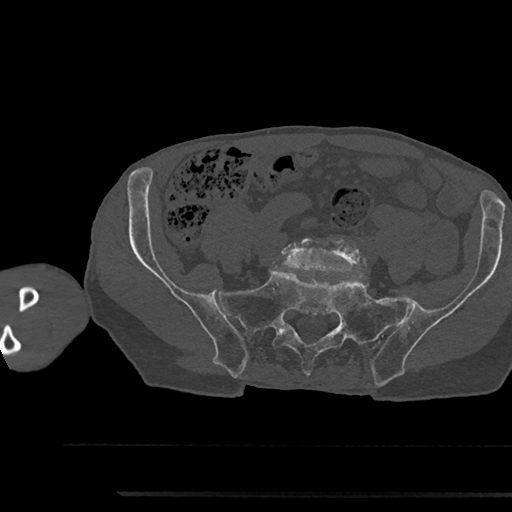
CT including the spine, one axial slice; position 298 of 797 along the scan axis; reconstruction kernel Br40s/3; 120 kVp; bone window (W 1800 / L 400 HU); 0.5 mm slice thickness; 512 × 512 image matrix. Male patient, age 79 years. From the clinical record (not read from this slice): primary cancer: prostate.
Structures marked on this image (semi-automatically segmented with operator editing):
- L5 vertebra: bounding box (x1, y1, x2, y2) in pixels: (281, 237, 367, 274)